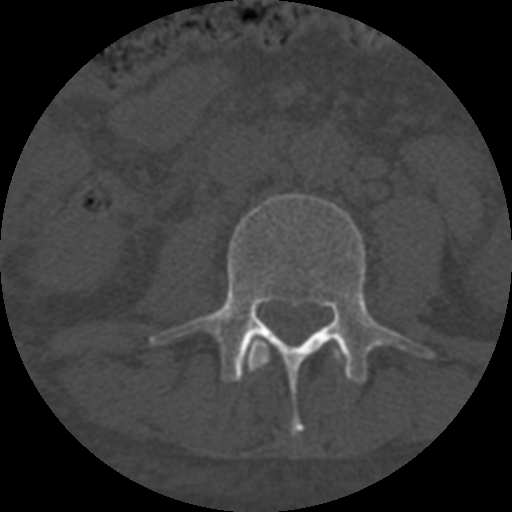
CT including the spine, one axial slice; slice 239 of 708 in the series (ordered by position); one of 3 acquisitions stored at this slice position; bone window (W 1800 / L 400 HU); 512 × 512 image matrix. Patient age 55 years. From the clinical record (not read from this slice): primary cancer: colon; vertebrae with lytic lesions (as recorded): T12, L1, L5.
Annotated regions visible in this slice (semi-automatic segmentation, software-assisted and operator-edited):
- L2 vertebra: box from (x=247, y=340) to (x=341, y=373) px
- L3 vertebra: (x=150, y=193)–(x=437, y=434)